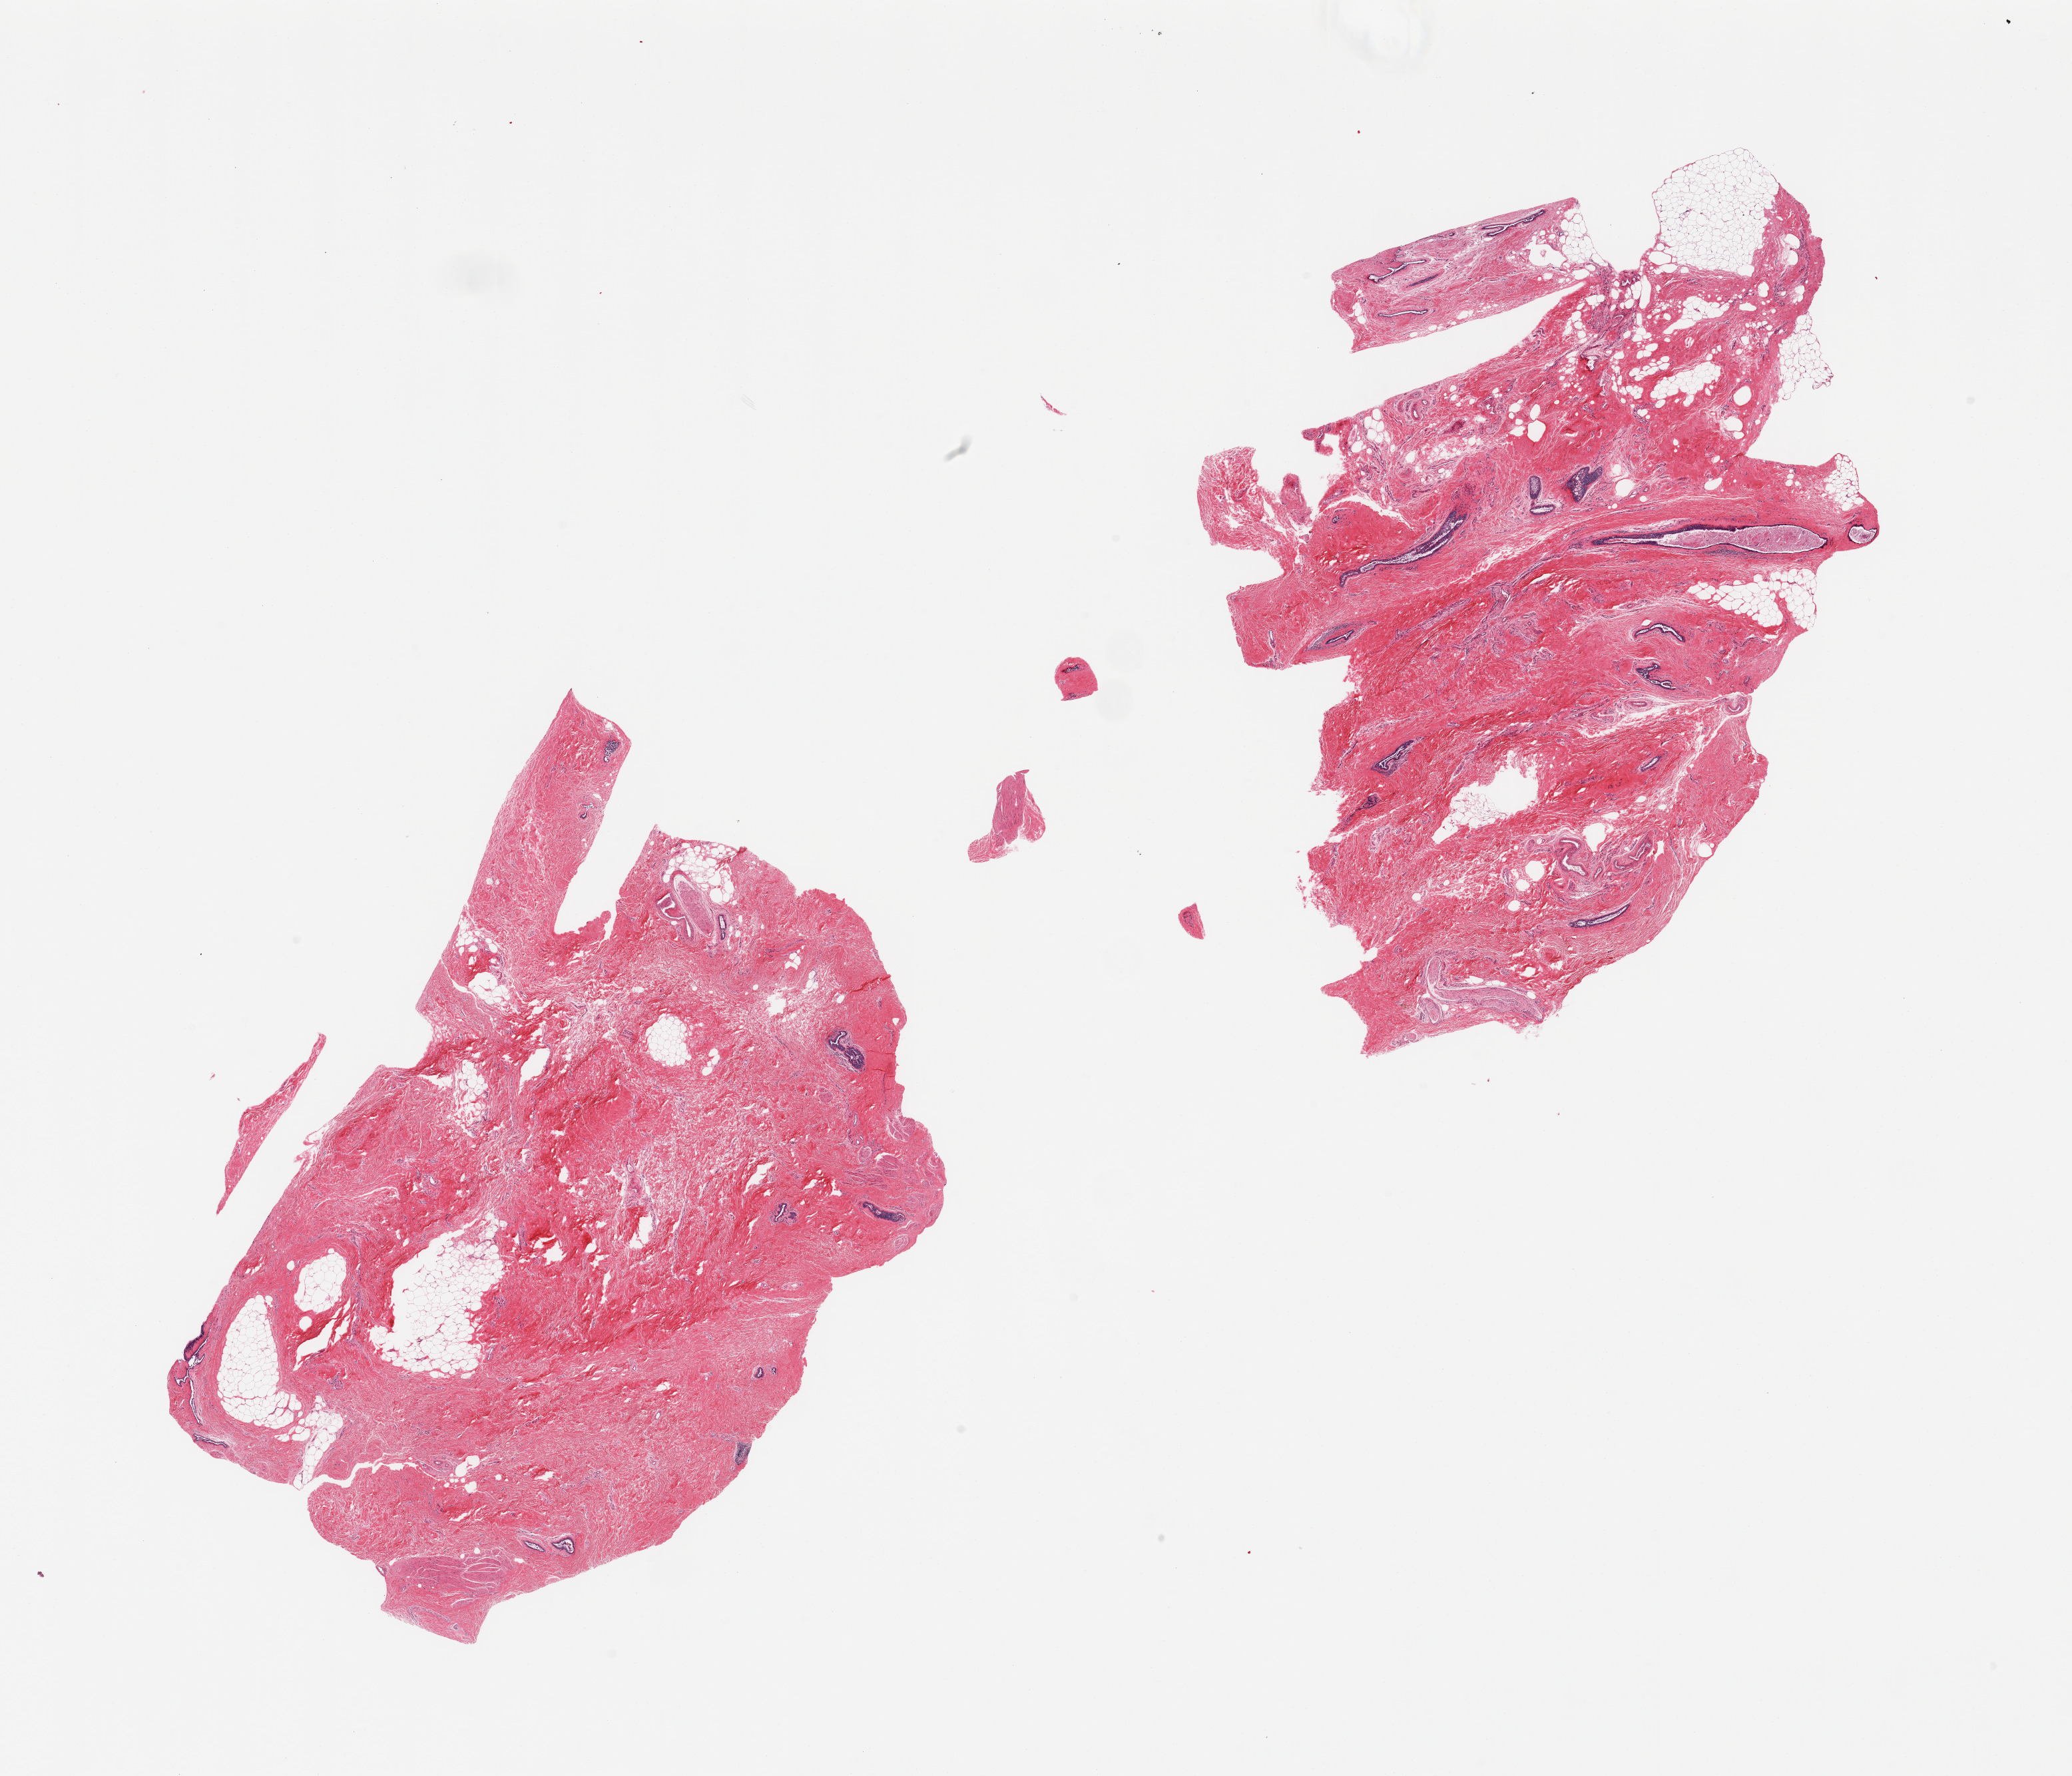
Digitized haematoxylin and eosin-stained section, brightfield — shown as a low-resolution overview of the whole scanned area (about 24.6 x 21.1 mm), PAXgene-fixed paraffin-embedded (PFPE) section, target tissue: breast, tissue donor sample. Donor sex: male.
- review note (as recorded): 2 pieces, gynecomastoid stromal and ductal hyperplasia